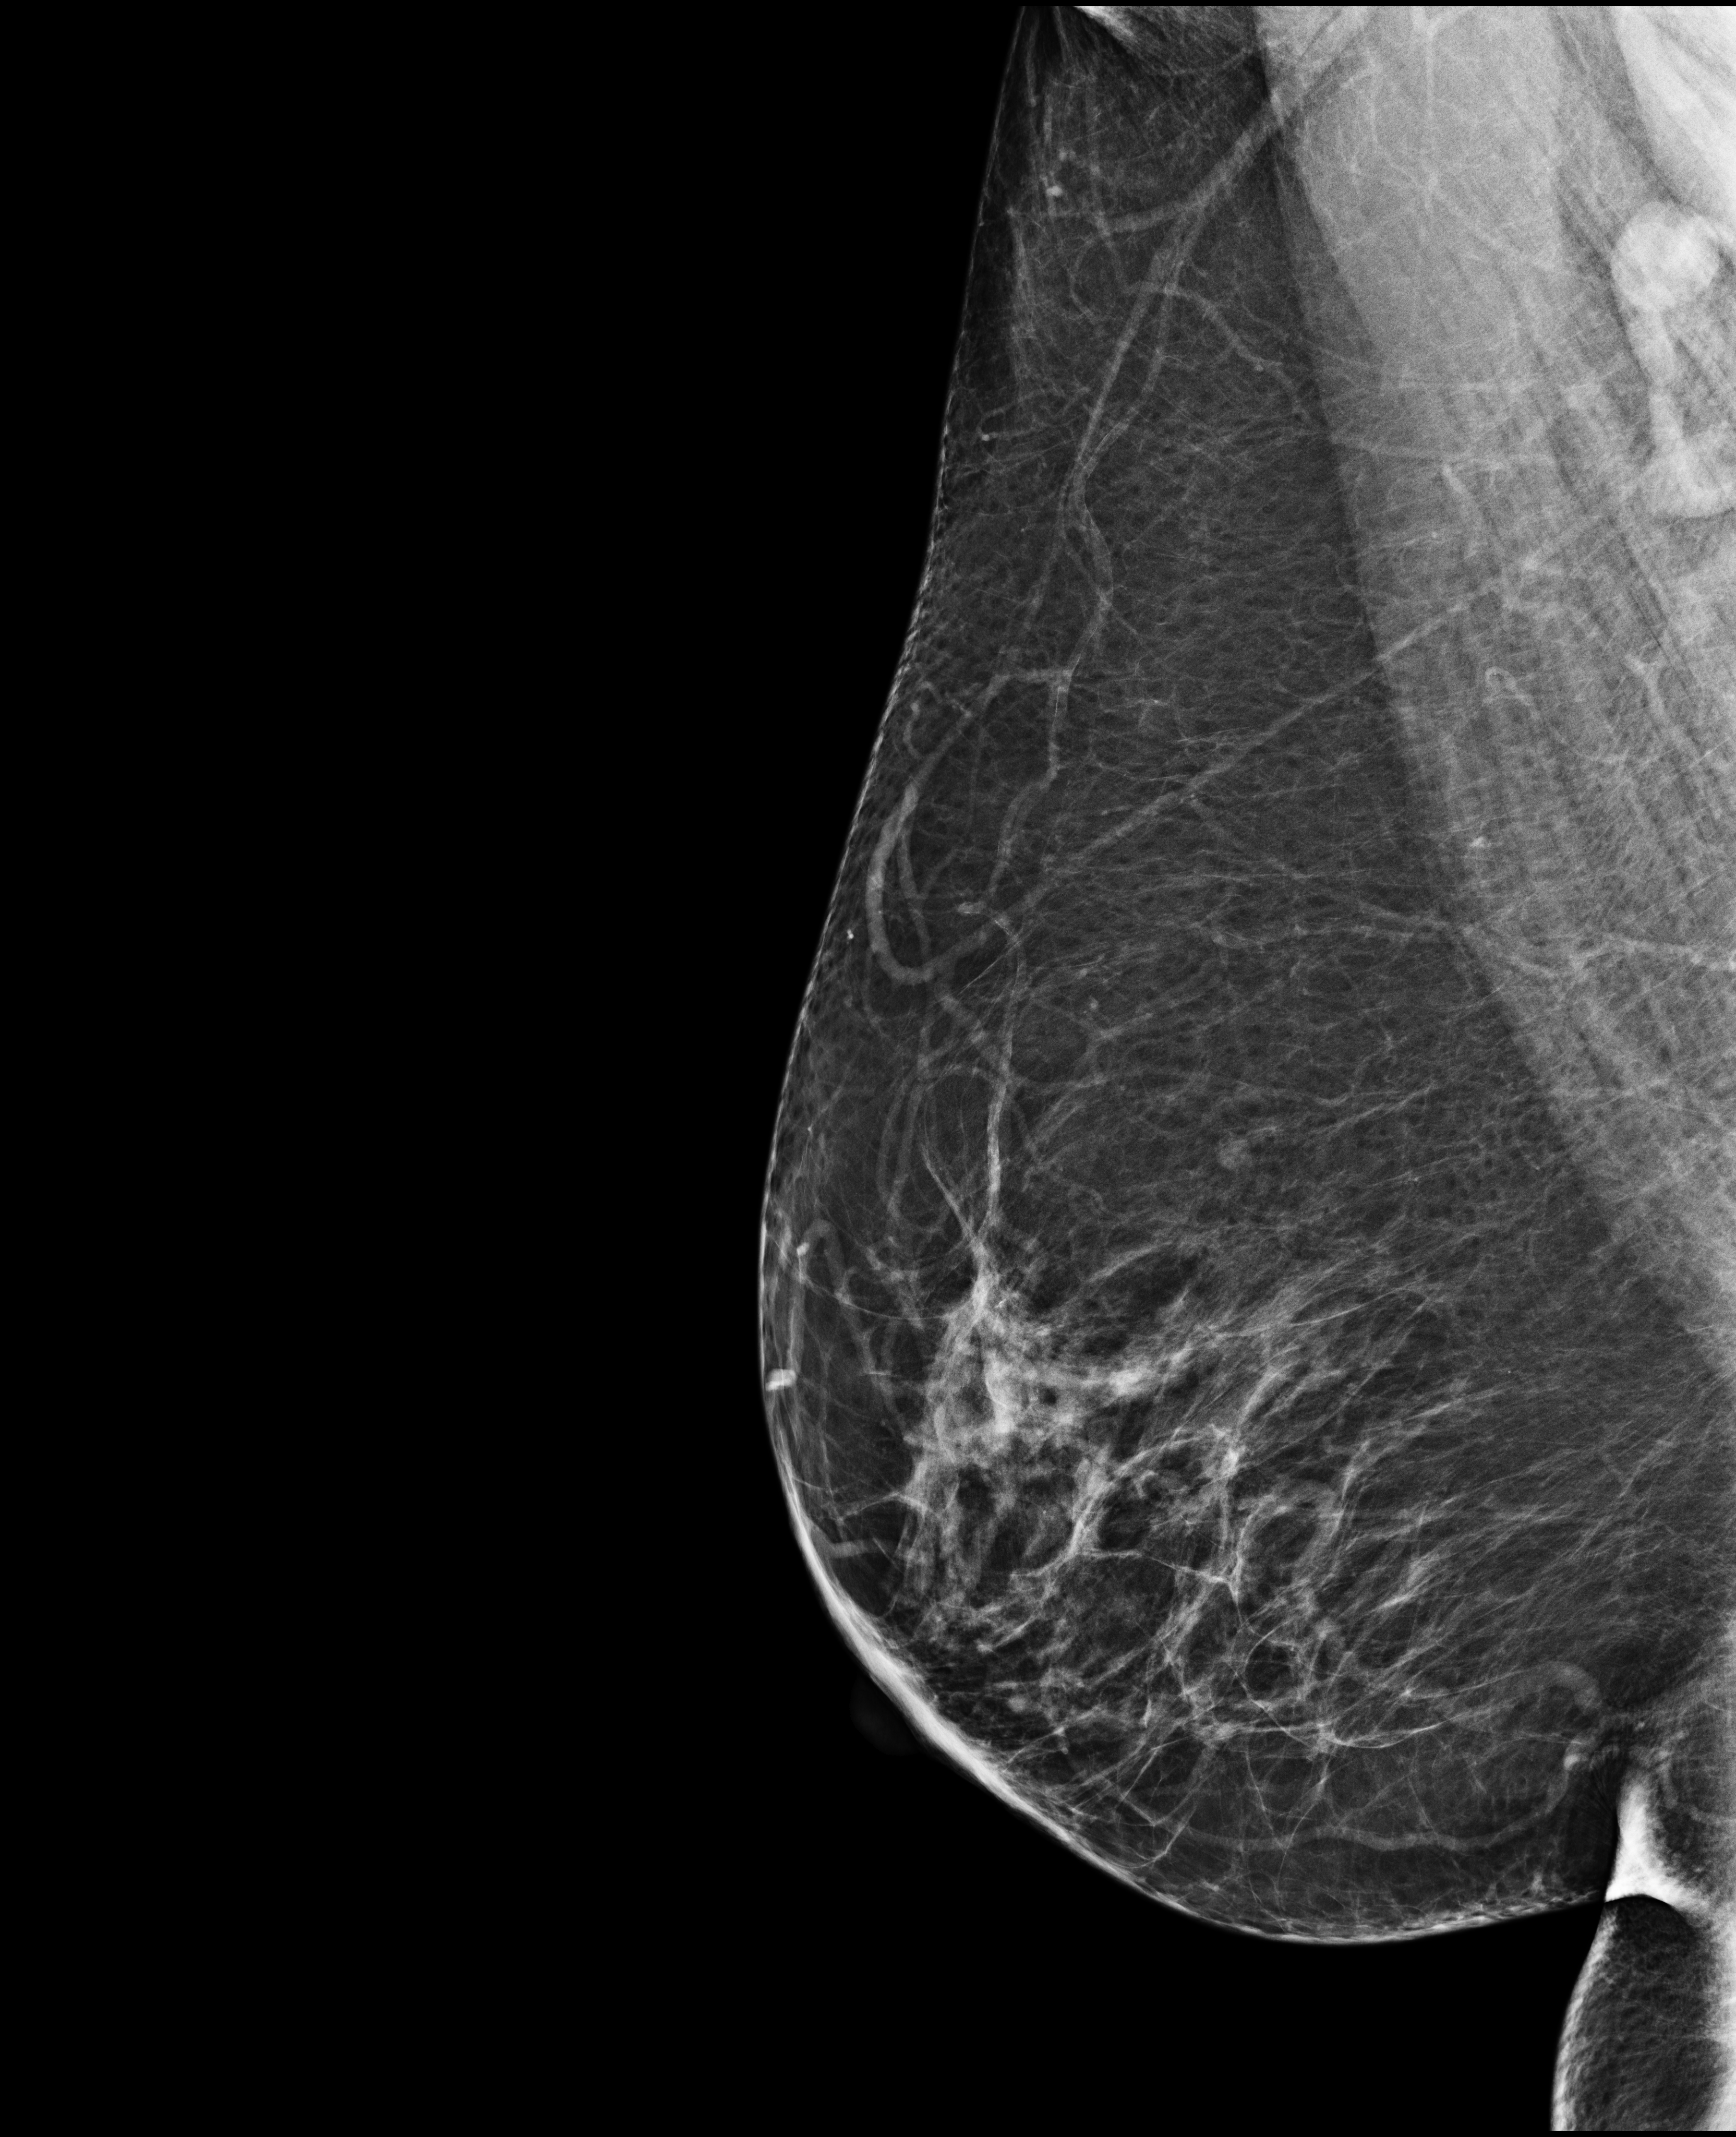
Full-field digital mammogram (FFDM); right breast; medio-lateral oblique projection; annual screening mammography examination. Female patient, age 61 years.
- breast density at the screening exam (both breasts): heterogeneously dense (BI-RADS density category c)
- final BI-RADS category for the screening round (tomosynthesis exam, both breasts): category 1
- recall: no recall after this screen